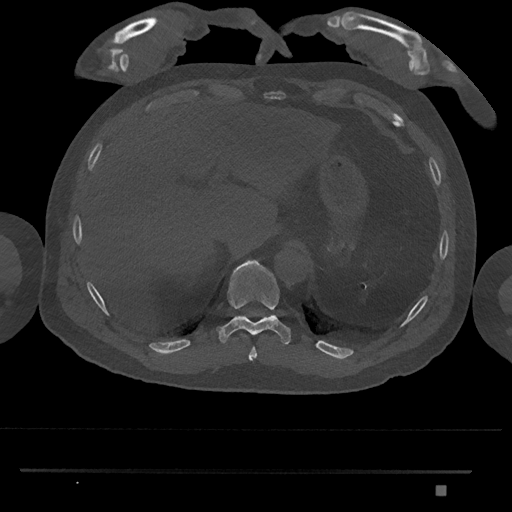
CT including the spine, one axial slice; position 1000 of 1134 along the scan axis; reconstruction kernel Br40s/3; bone window (W 1800 / L 400 HU); 512 × 512 image matrix. Male patient, age 65 years. Case-level facts recorded for this patient, not image findings: primary cancer: prostate.
Annotated regions visible in this slice (semi-automatically segmented with operator editing):
- T10 vertebra: bounding box <216,259,291,346> (left, top, right, bottom; pixels)
- T11 vertebra: <238,316,242,317>
- T9 vertebra: <248,347,257,361>